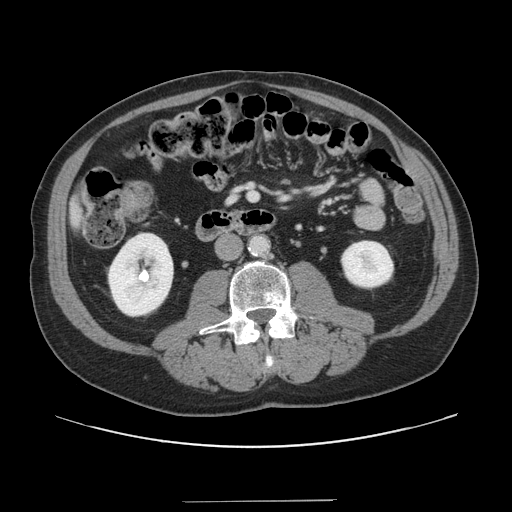
Contrast-enhanced abdominal CT, one axial slice; slice 34 of 151 in the series (ordered by position); 120 kVp; intravenous contrast given; soft-tissue window (W 400 / L 40 HU); 2.5 mm slice thickness; 512 × 512 image matrix, field of view 399 × 399 mm. Male patient, age 63 years. Case-level facts recorded for this patient, not image findings: diagnosis: colorectal cancer liver metastases, imaged before liver resection; multiple liver metastases: no; largest metastasis: 2.1 cm.
Annotated regions visible in this slice (manually delineated by an expert):
- liver: bounding box [x1, y1, x2, y2] px = [72, 202, 81, 228]
- planned liver remnant (the part of the liver to remain after resection): [72, 202, 82, 228]
- portal vein (with intrahepatic branches): [249, 193, 258, 200]